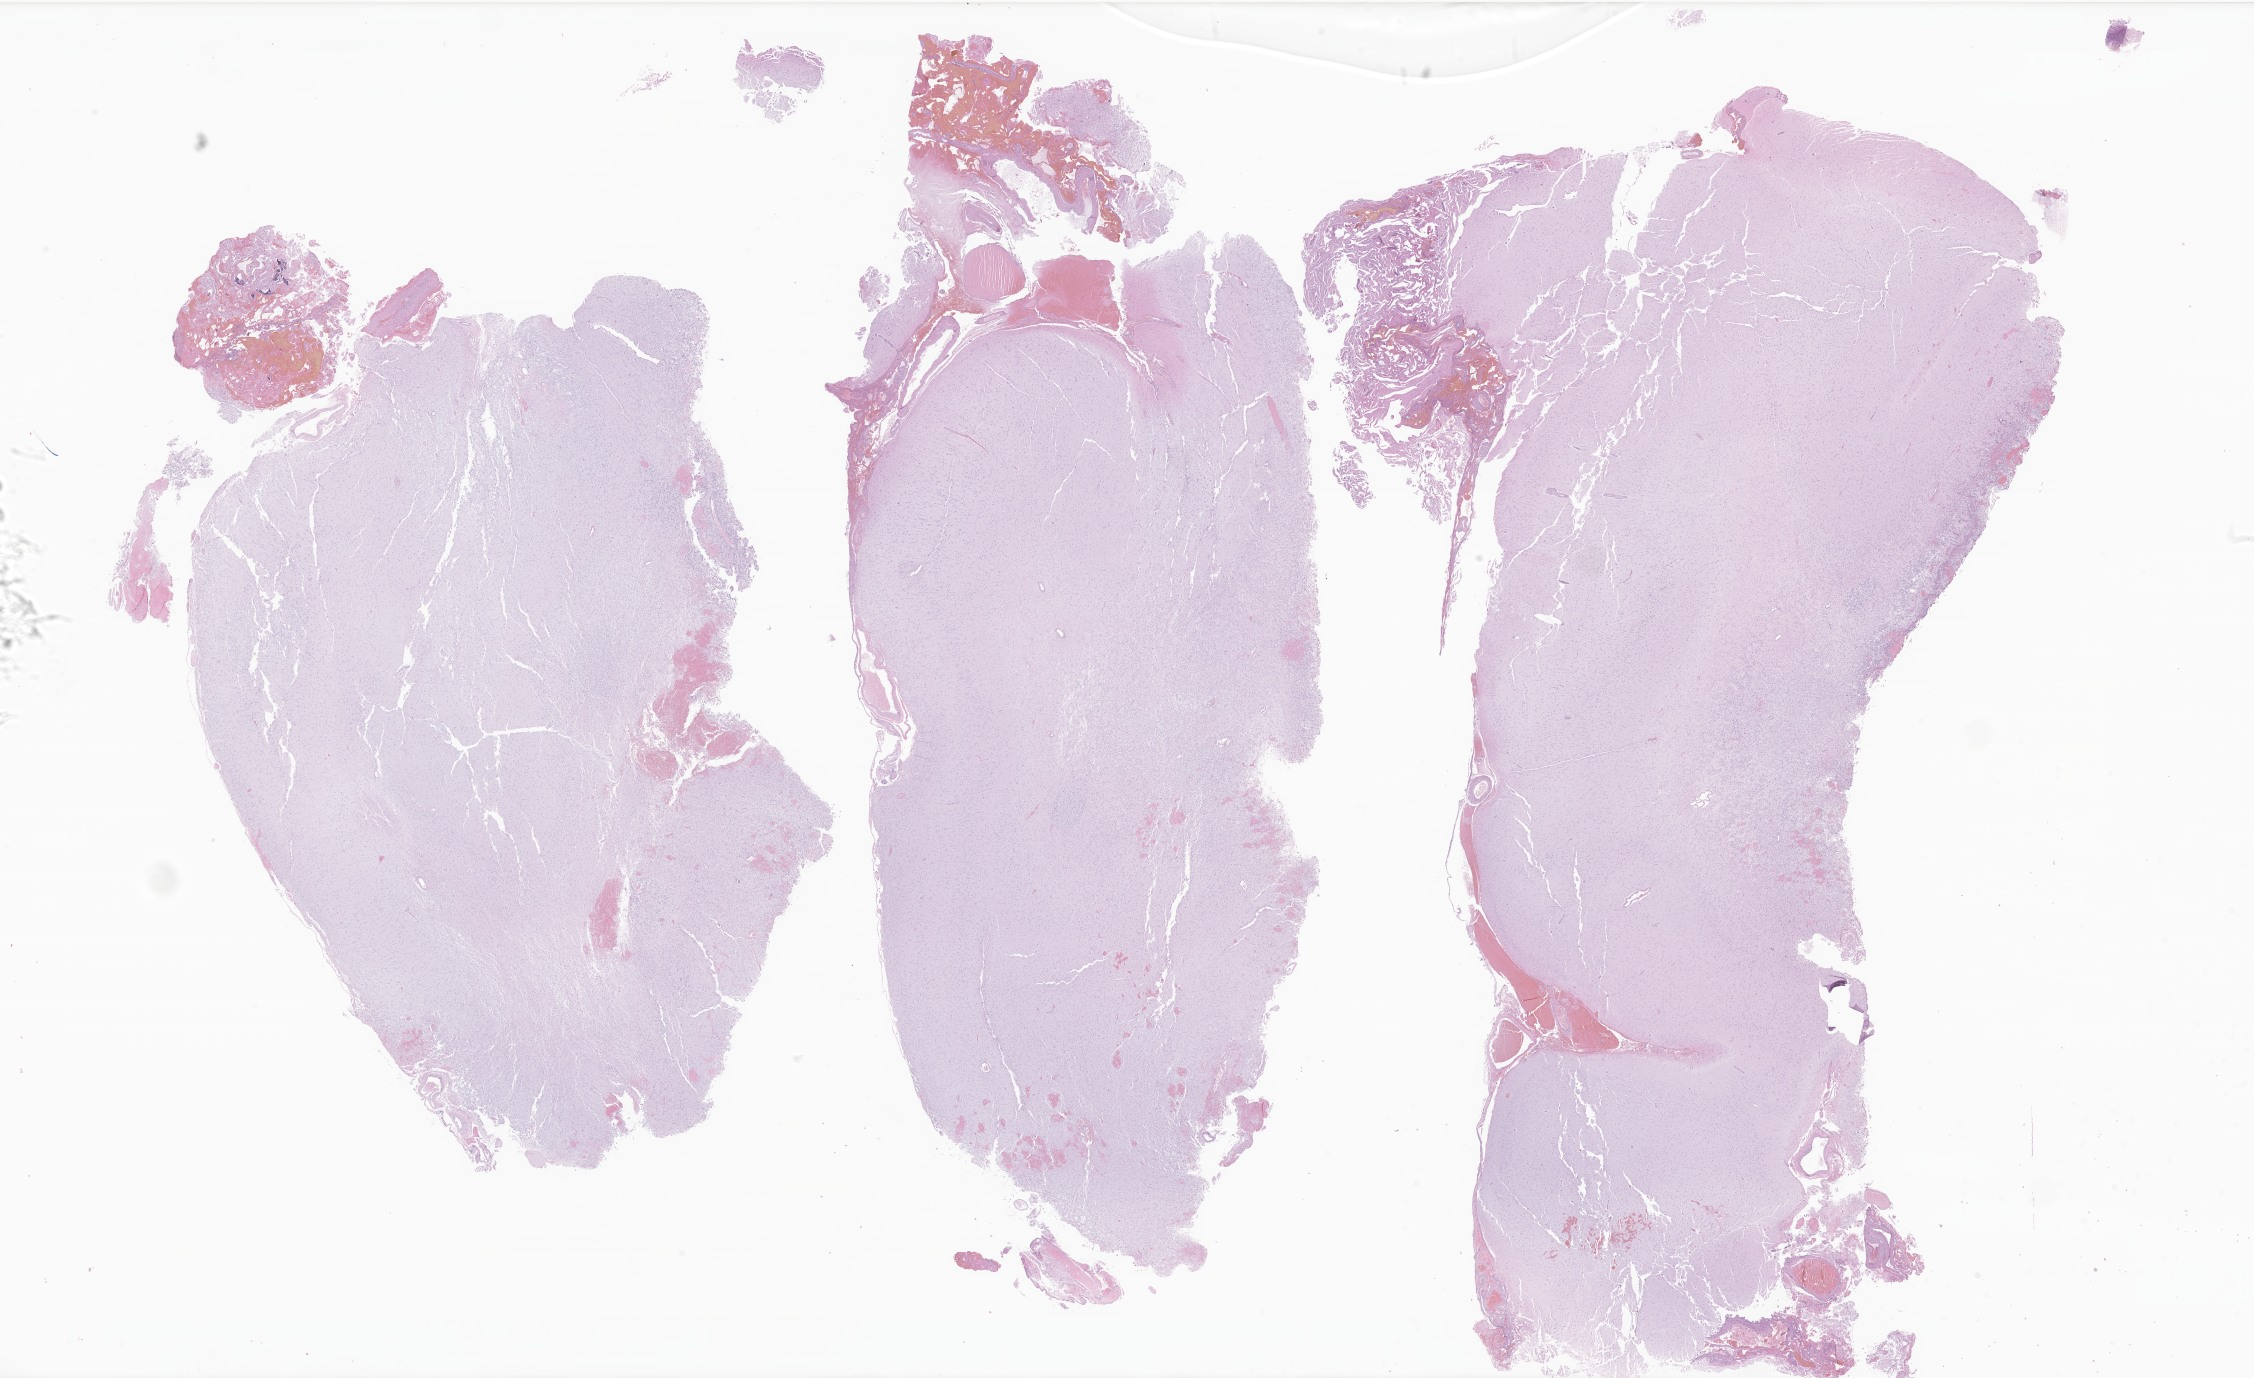
H&E whole-slide image of tumor tissue from the occipital lobe, whole scanned area (about 38.0 x 23.2 mm) shown as a low-resolution overview. Male patient, age 89 months (7 years 5 months).
Specimen: formalin-fixed, paraffin-embedded (FFPE) tissue.